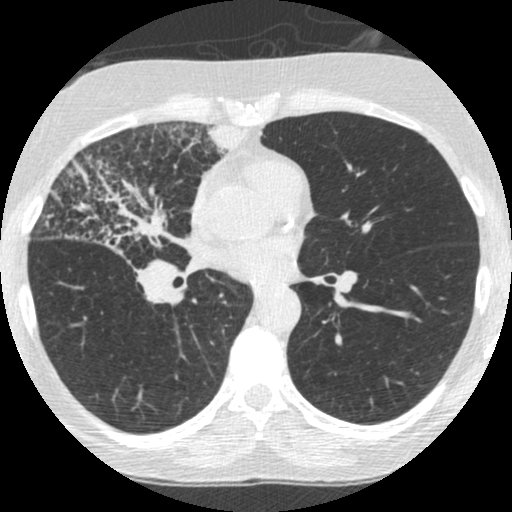
Low-dose screening chest CT, one axial slice. Position 135 of 253 along the scan axis. Reconstruction kernel STANDARD. 120 kVp. Lung window (W 1500 / L -600 HU). 1.25 mm slice thickness. 512 × 512 image matrix, field of view 294 × 294 mm.
Annotated regions visible in this slice (outlined manually by an expert reader):
- lesion 2 (tumor, hilum of right lung): bounding box [x1, y1, x2, y2] px = [35, 147, 193, 258]
- lesion 4 (tumor, upper lobe of right lung): [206, 123, 252, 161]